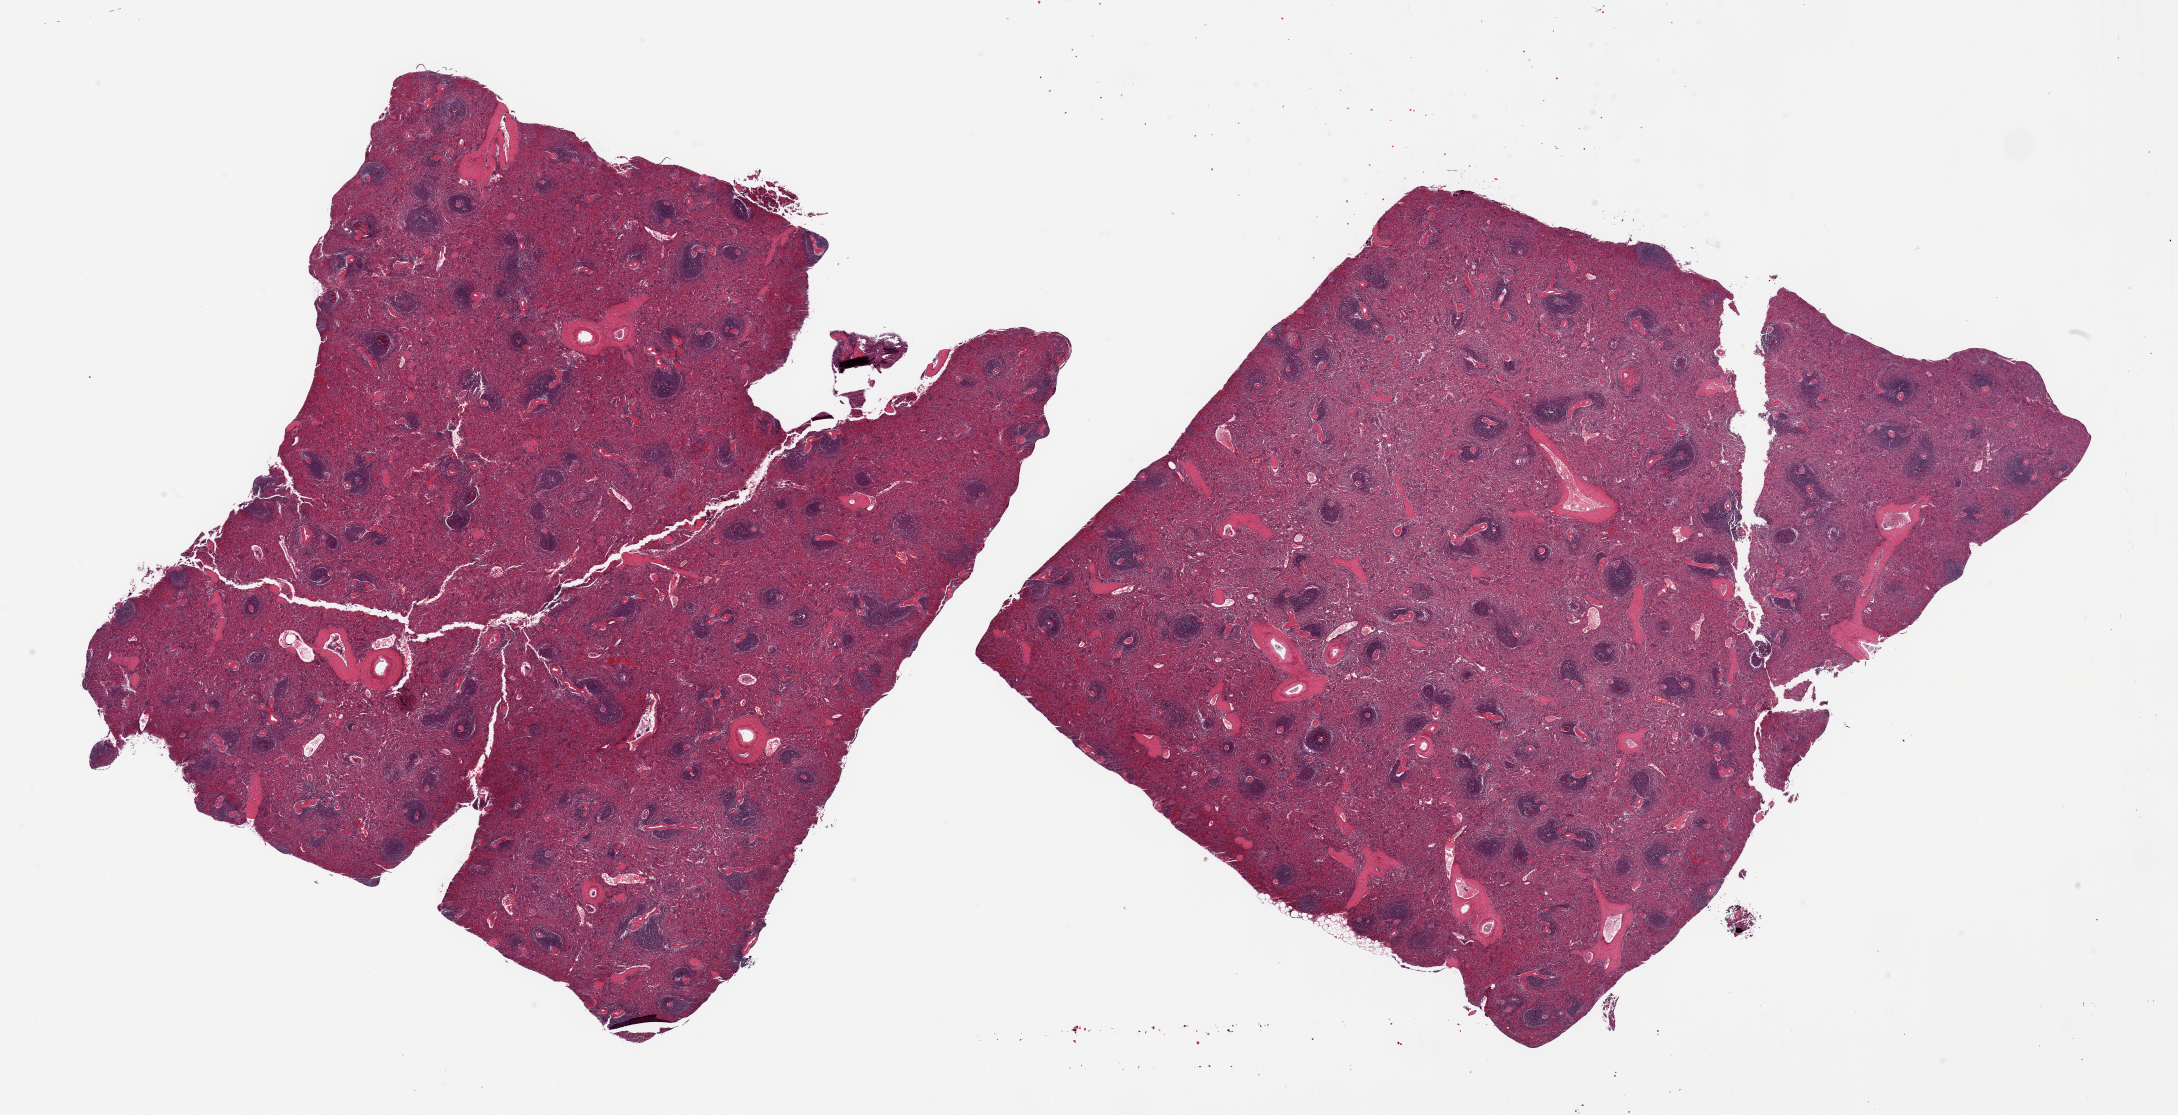
Digitized H&E-stained section, brightfield — low-resolution overview of the scanned area, about 34.5 x 17.6 mm; PAXgene-fixed, paraffin-embedded tissue; section of spleen (target tissue); tissue donor sample. Donor: female.
Pathologist's review note for this sample: 2 pieces, no abnormalities.